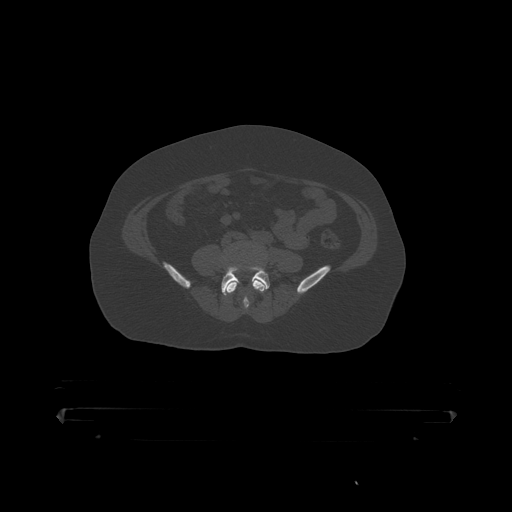
CT including the spine, one axial slice; position 50 of 390 along the scan axis; reconstruction kernel STANDARD; bone window (W 1800 / L 400 HU); 512 × 512 image matrix. Patient: male, 60 years. From the clinical record (not read from this slice): primary cancer: prostate.
Structures marked on this image (semi-automatically segmented with operator editing):
- L4 vertebra: bounding box [x1, y1, x2, y2] px = [226, 244, 267, 310]
- L5 vertebra: [221, 267, 280, 296]